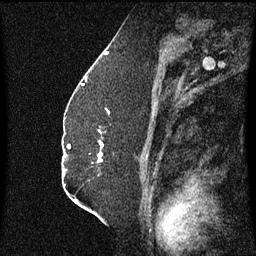
Breast MRI (dynamic contrast-enhanced), one sagittal slice; position 36 of 60 along the scan axis; dynamic contrast-enhanced series, image 2 of 3 at this slice position (ordered by acquisition); 1.5 T; TE 4.2 ms, TR 8.4 ms; 2.3 mm slice thickness; 256 × 256 image matrix, field of view 200 × 200 mm. Female patient, age 52 years. From the clinical record (not read from this slice): setting: breast cancer imaged before/during neoadjuvant chemotherapy; receptor status: HR-positive, HER2-negative.
Annotated regions visible in this slice (semi-automatically segmented with operator editing):
- analysis volume of interest (the breast-tissue region the enhancement analysis was run in; not a lesion): bounding box [x1, y1, x2, y2] px = [97, 130, 103, 163]
- tumour enhancement mask (voxels above the 70 % enhancement threshold inside the analysis volume of interest): [98, 132, 103, 163]